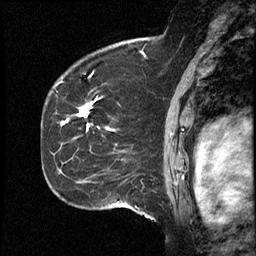
Breast MRI (dynamic contrast-enhanced), one sagittal slice. Slice 33 of 46 in the series (ordered by position). Dynamic contrast-enhanced study with each time point stored as its own series, time point 2 of 4 at this slice position (early post-contrast, ordered by acquisition time). 1.5 T. TE 4.2 ms, TR 18.3 ms. 3 mm slice thickness. 256 × 256 image matrix, field of view 200 × 200 mm. From the clinical record (not read from this slice): setting: breast cancer imaged before/during neoadjuvant chemotherapy; receptor status: HR-positive, HER2-negative.
Outlined on this slice (semi-automatically segmented with operator editing):
- analysis volume of interest (the breast-tissue region the enhancement analysis was run in; not a lesion): box from (x=64, y=71) to (x=111, y=209) px
- tumour enhancement mask (voxels above the 100 % enhancement threshold inside the analysis volume of interest): (x=79, y=106)–(x=91, y=128)